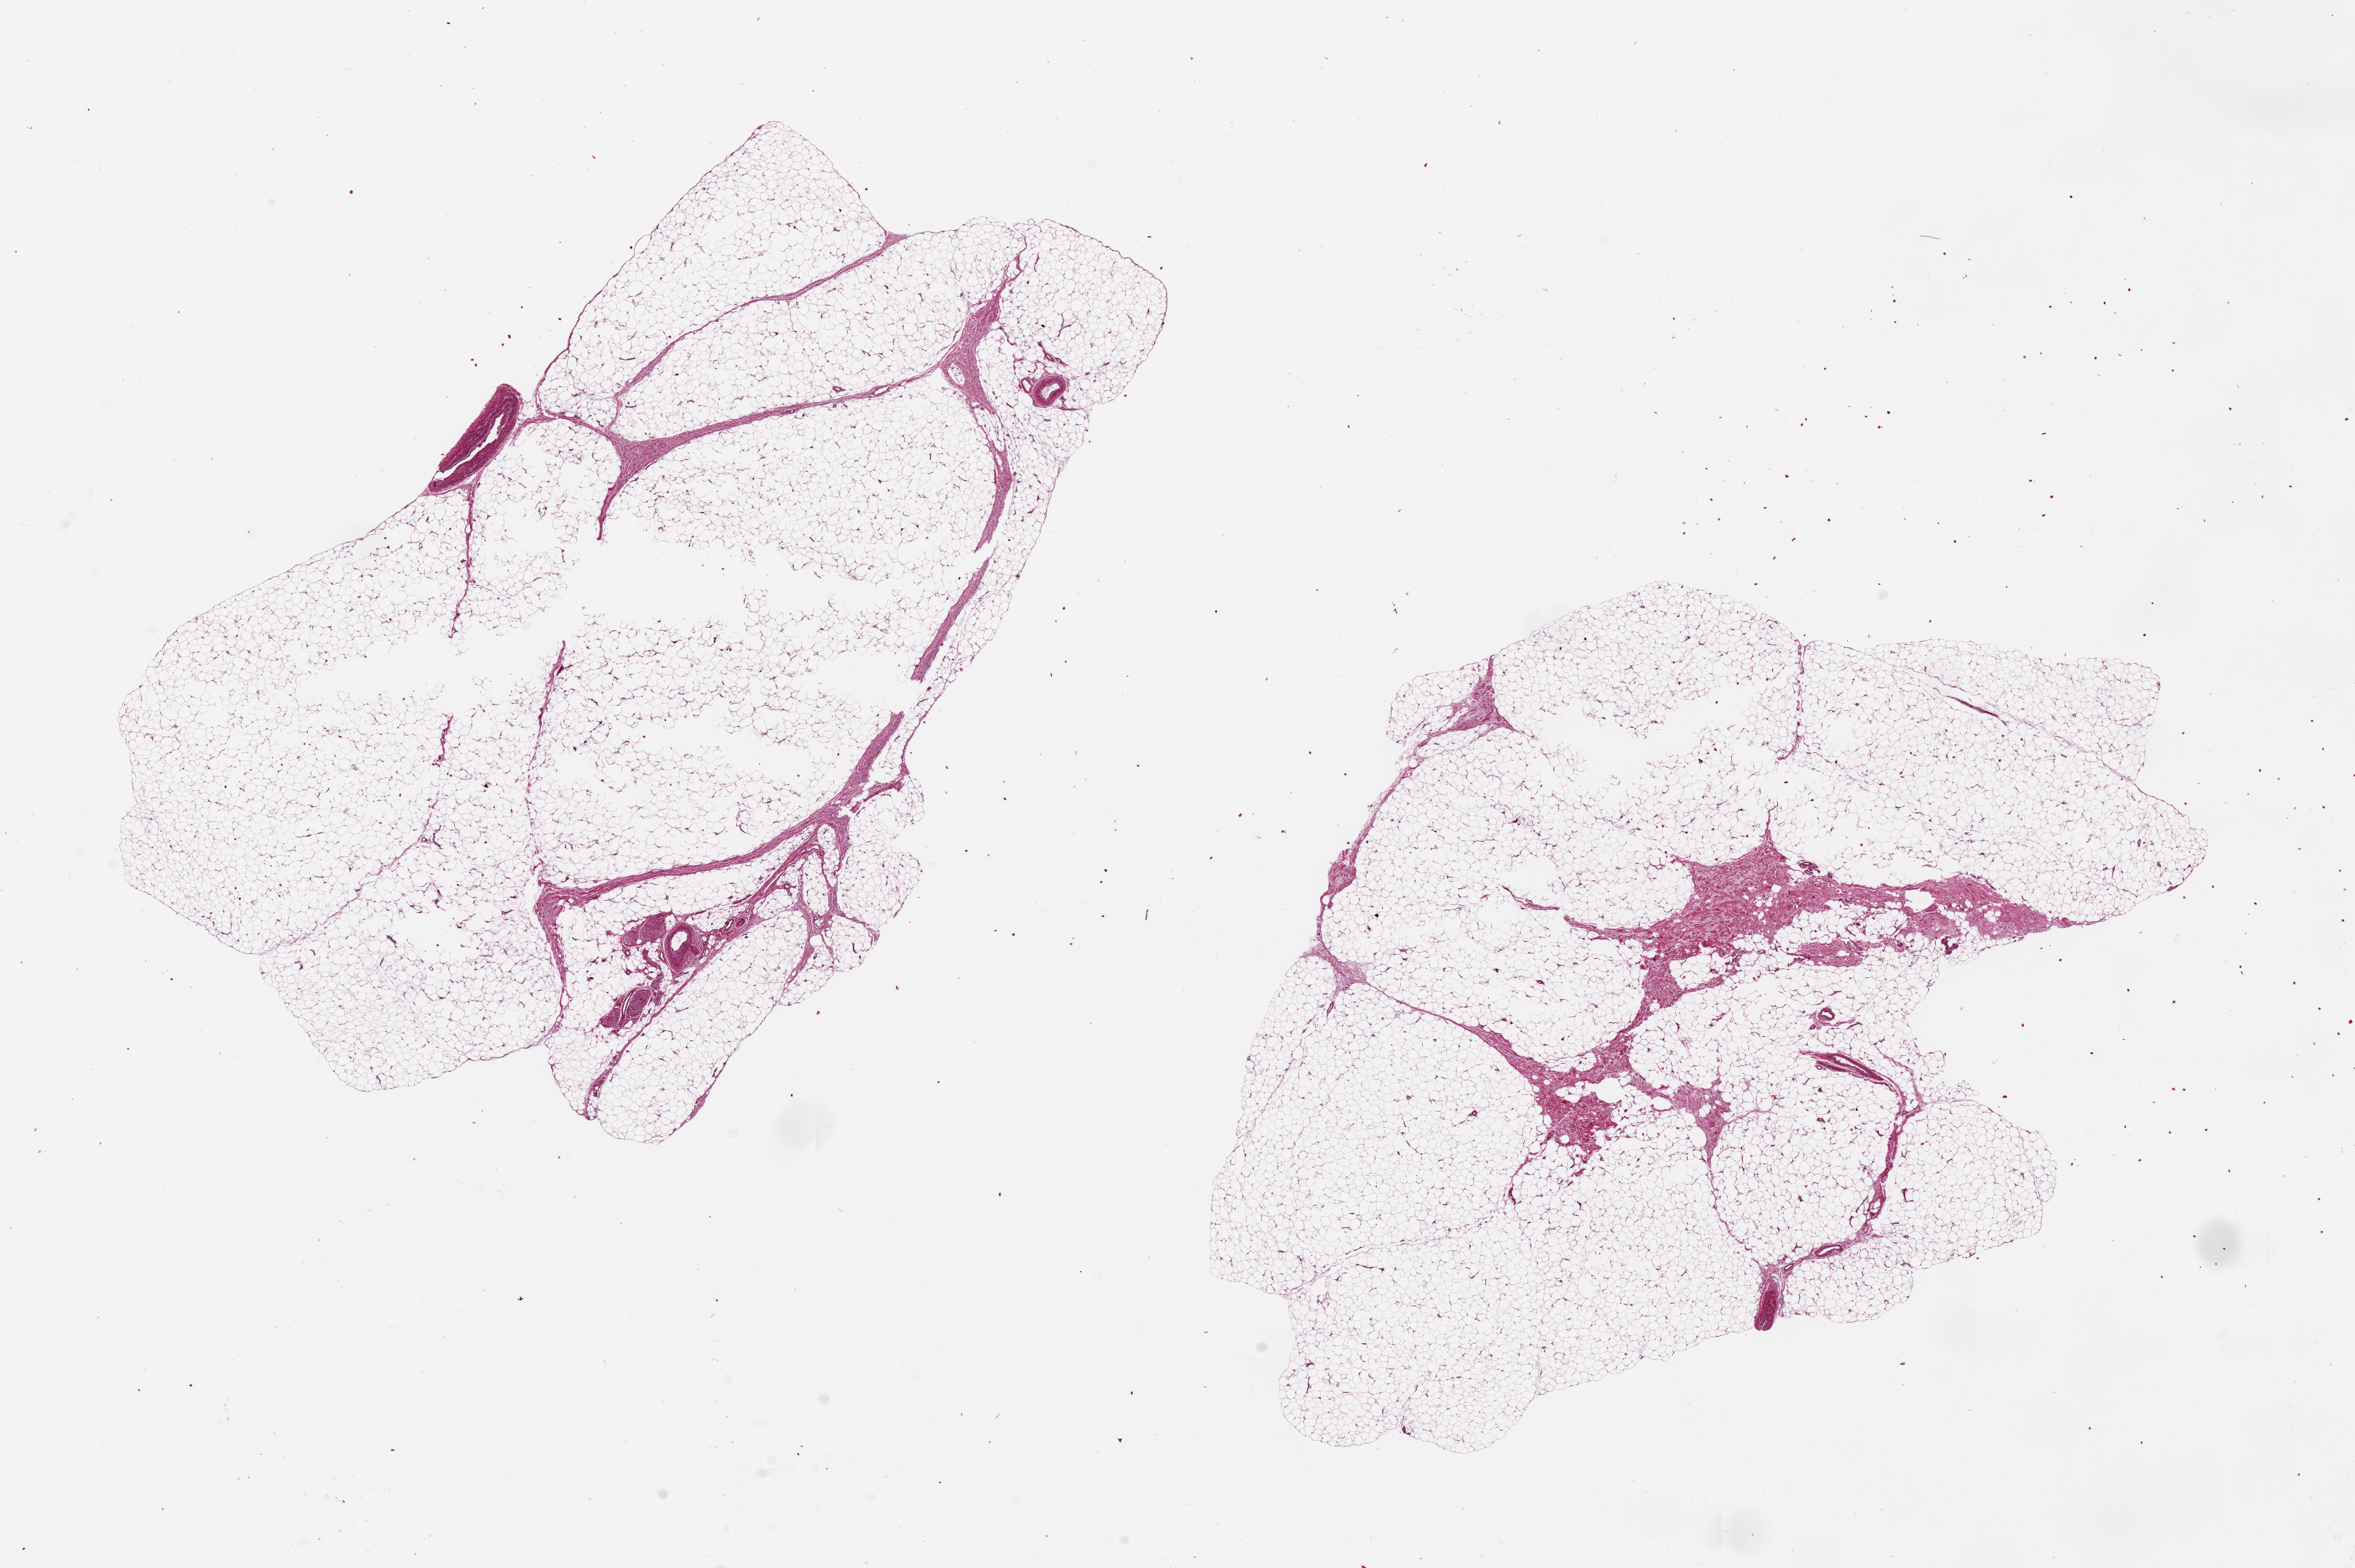
Whole-slide image, hematoxylin and eosin (H&E) stain — whole scanned area (about 25.6 x 17.0 mm, slide scanned at 20x) shown as a low-resolution overview; PAXgene-fixed, paraffin-embedded tissue; sampled site (target tissue): adipose tissue; tissue donor sample. Female donor.
Pathologist's review note for this sample: 2 pieces, 12x8.5 & 12x9mm.